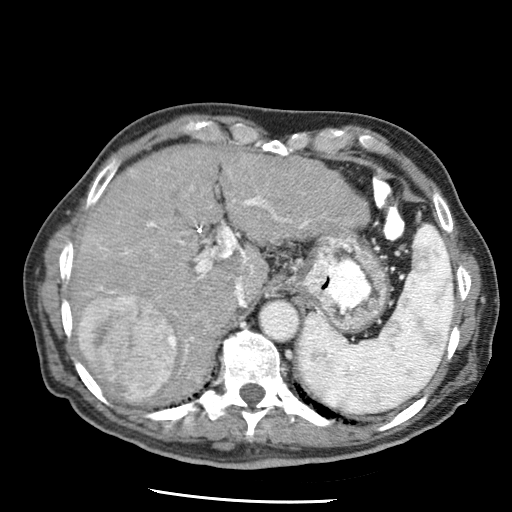
Contrast-enhanced abdominal CT (liver protocol), one axial slice. Slice 44 of 79 in the series (ordered by position). Soft-tissue window (W 400 / L 40 HU). 512 × 512 image matrix, field of view 320 × 320 mm. From the clinical record (not read from this slice): diagnosis: hepatocellular carcinoma (patient treated with transarterial chemoembolisation; whether this scan precedes or follows treatment is not stated here); TNM stage (as recorded): Stage-IIIA.
Outlined on this slice (semi-automatic segmentation, software-assisted and operator-edited):
- liver parenchyma outside the tumour (the mass and vessels are separate outlines, so this box may not span the whole liver): bounding box <68,146,370,402> (left, top, right, bottom; pixels)
- mass: <77,296,176,400>
- liver vessels: <98,171,310,314>